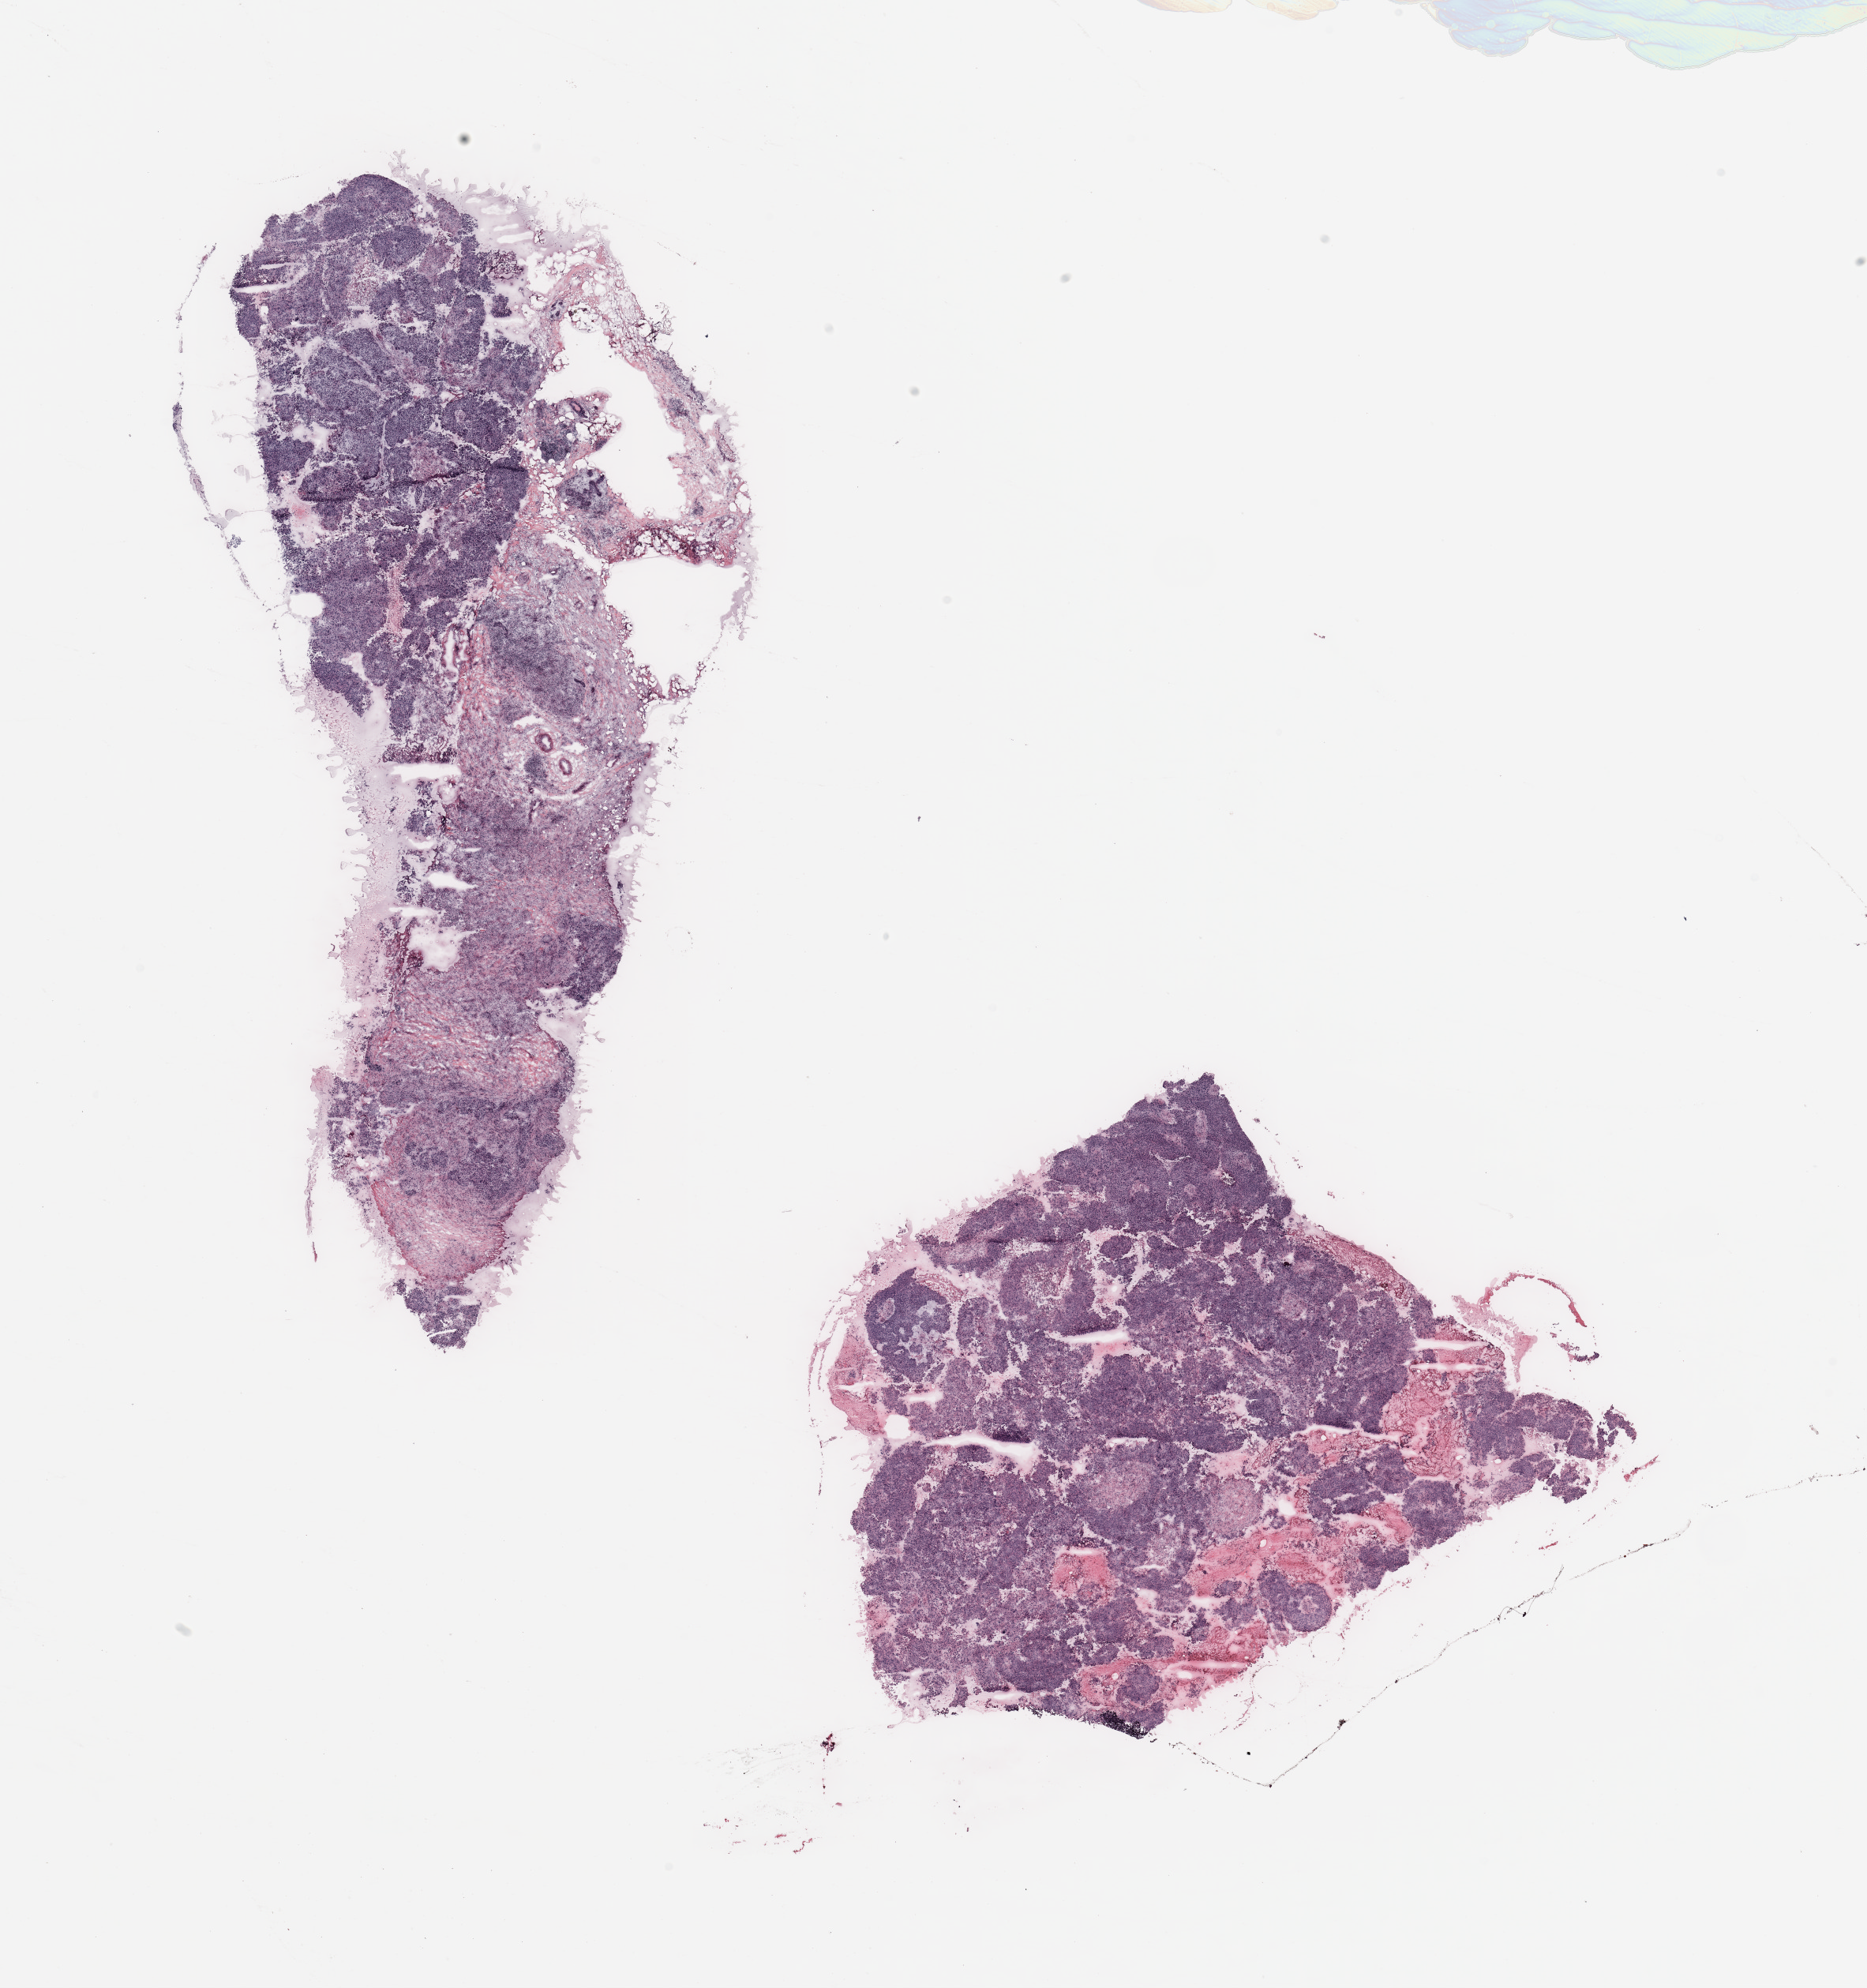
H&E-stained whole-slide image — shown as a low-resolution overview of the whole scanned area (about 18.7 x 19.9 mm, from a 20x scan); breast, tumour tissue. Female, 66 y/o.
Diagnosis: Infiltrating duct carcinoma, NOS. AJCC pathologic stage: IIIA.